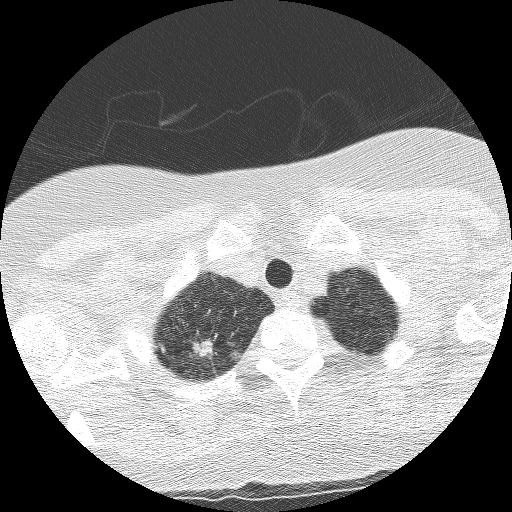
Low-dose screening chest CT, axial slice; third screening round (two years after baseline); lung window (W 1500 / L -600 HU); 2.5 mm slice thickness; lung (sharp) reconstruction kernel (BONE); 120 kVp; 512 × 512 image matrix, field of view 290 × 290 mm. Female, age 56 years at enrolment. Current smoker at enrolment.
Expert reader's lesion annotation, bounding box (x1, y1, x2, y2) in pixels: (166, 329, 222, 381). Screening reader's record for this exam (one nodule recorded; not confirmed to be the boxed lesion): non-calcified nodule or mass ≥4 mm, right upper lobe, 17 × 10 mm, spiculated (stellate) margins, mixed attenuation, pre-existing on the prior screen: yes; interval growth: yes. Later outcome: lung cancer diagnosed 24 days after this screen — large cell carcinoma, NOS, right upper lobe, poorly differentiated (G3), stage IB (AJCC 6th edition), 15 mm at pathology.